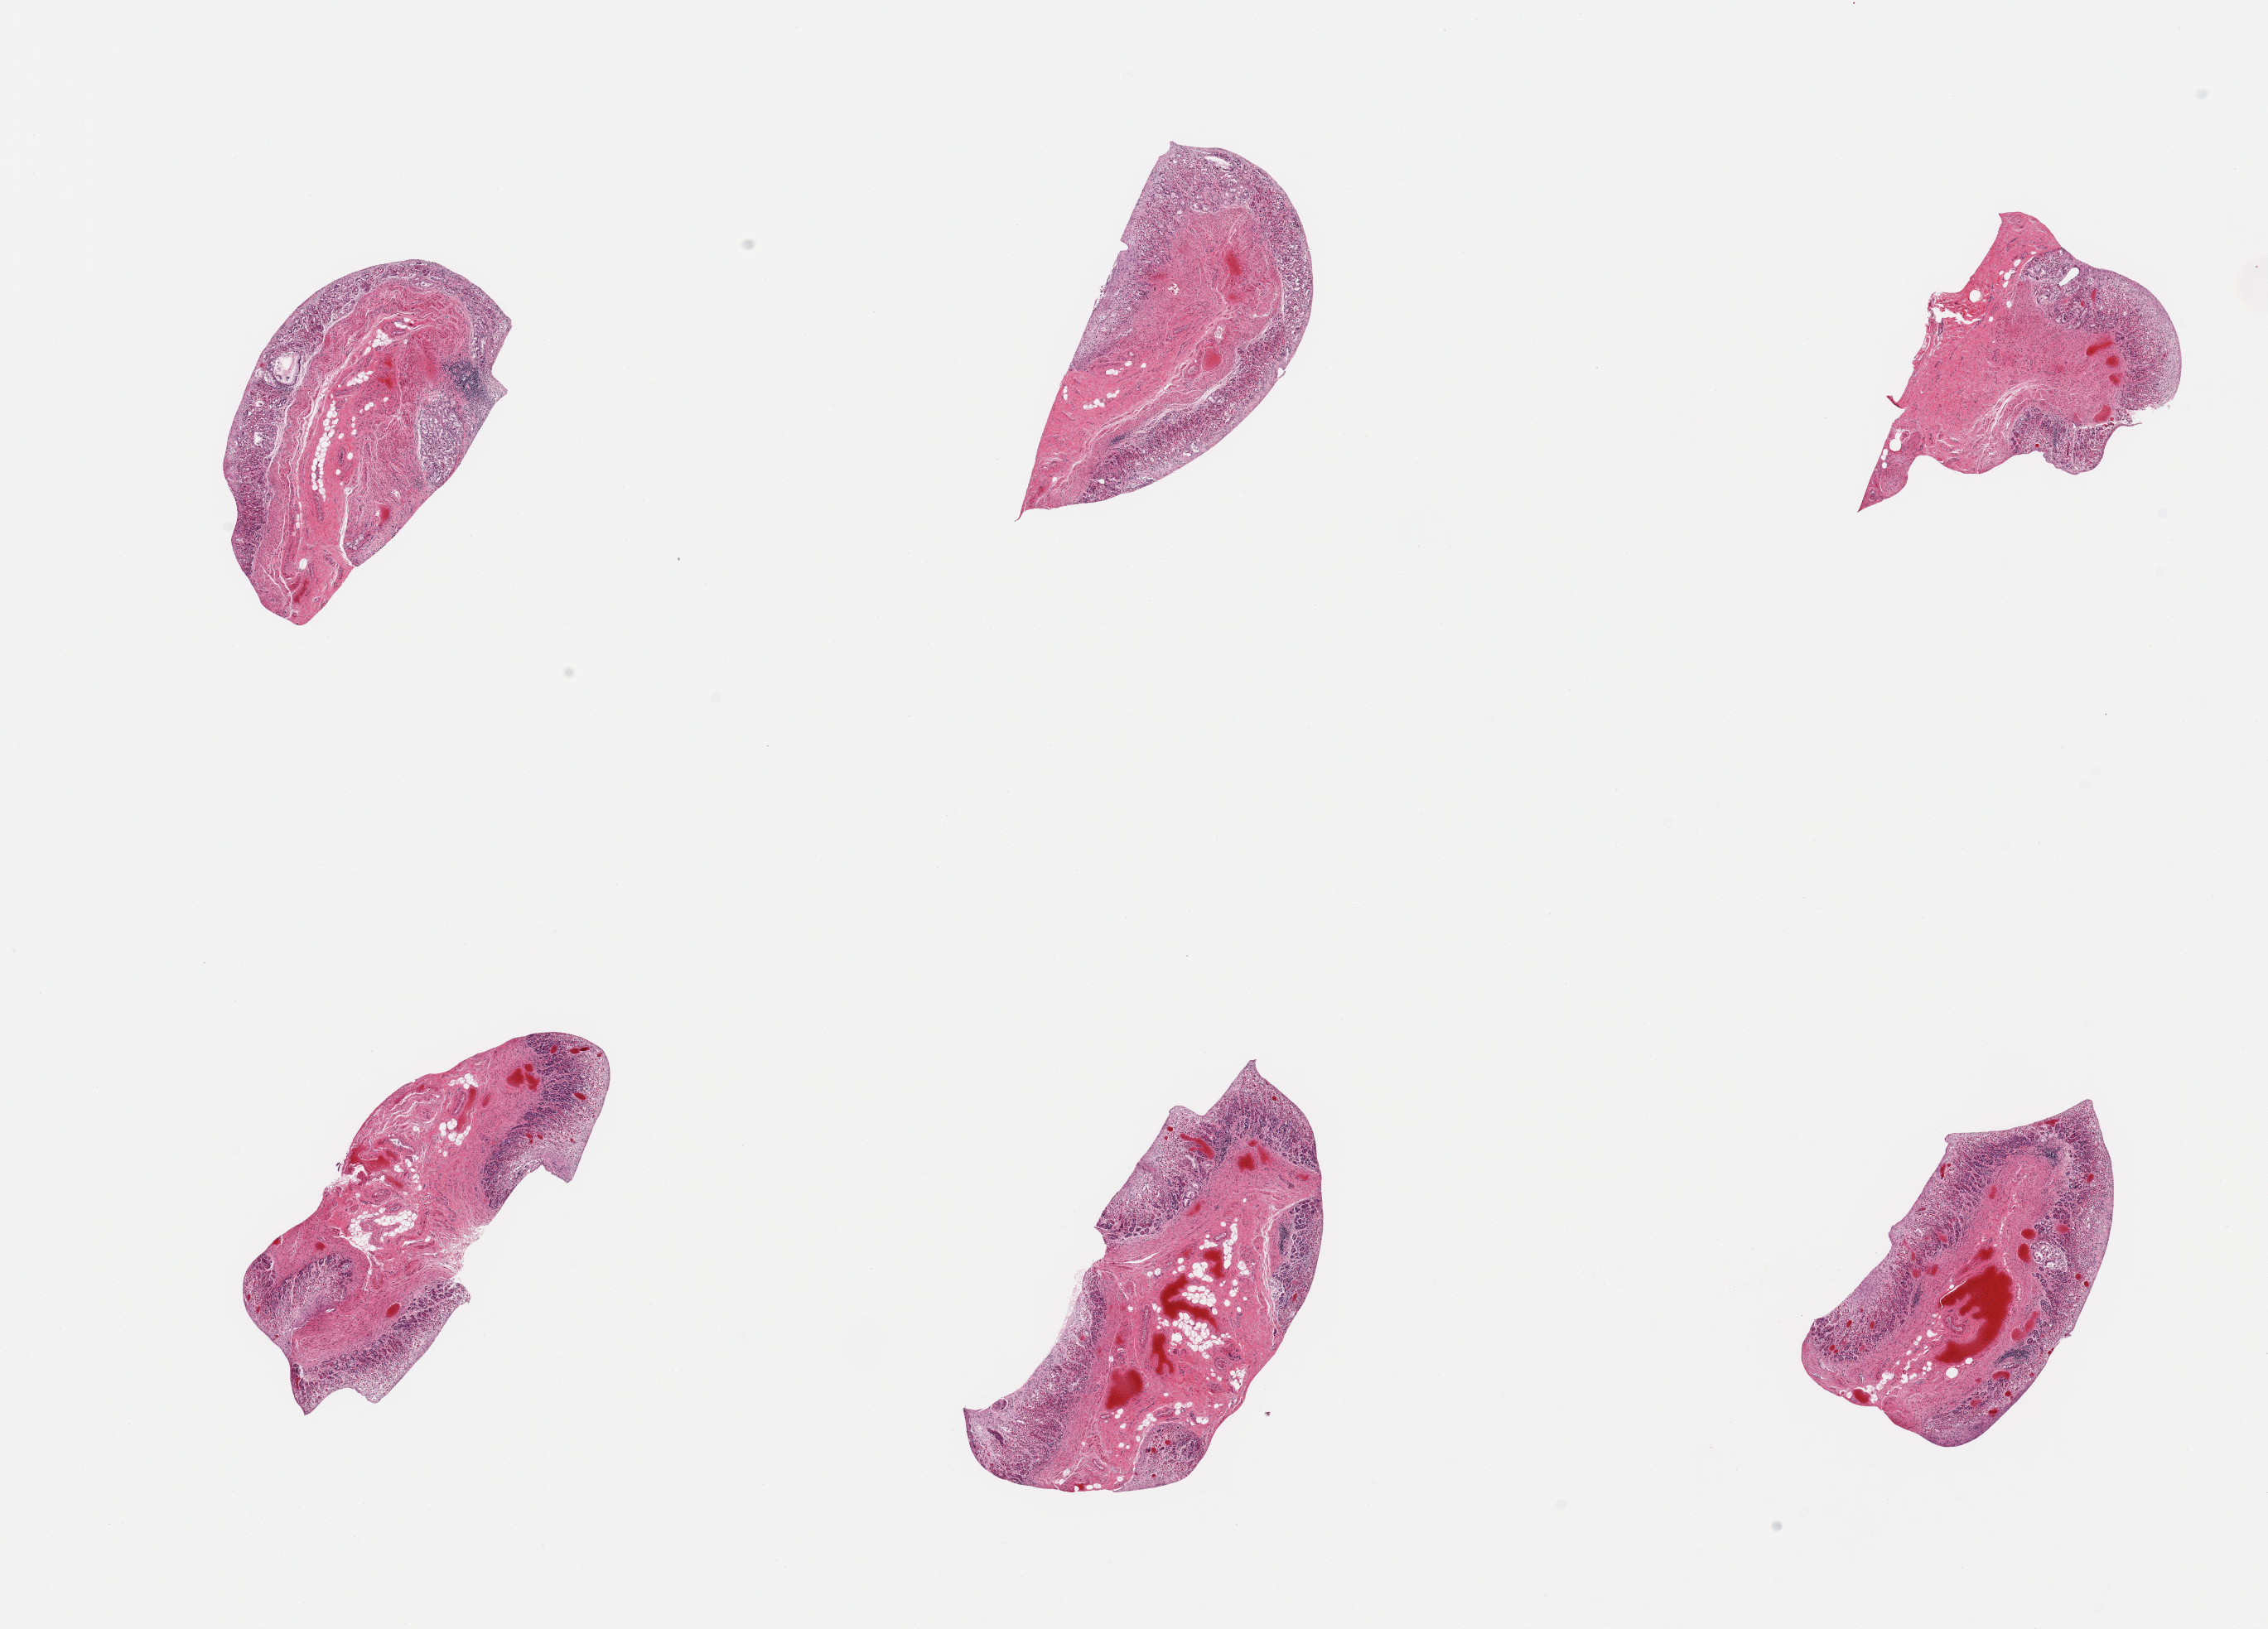
Digitized hematoxylin and eosin (H&E)-stained section, brightfield, shown as a low-resolution overview of the whole scanned area (about 21.7 x 15.6 mm, slide scanned at 20x). PAXgene-fixed paraffin-embedded (PFPE) section. Section of esophageal mucous membrane (target tissue). Donor tissue sample. Donor: female.
Review note (as recorded): 6 pieces; congested, partially autolyzed gastric mucosa.